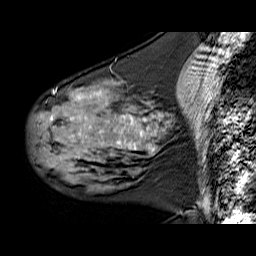
Breast MRI (dynamic contrast-enhanced), one sagittal slice. Dynamic contrast-enhanced series, time point 2 of 6 at this slice position (early post-contrast). 1.5 T. TE 6.3 ms, TR 32.9 ms. 256 × 256 image matrix, field of view 200 × 200 mm. Female patient. From the clinical record (not read from this slice): setting: breast cancer imaged before/during neoadjuvant chemotherapy; receptor status: HER2-positive.
Annotated regions visible in this slice (semi-automatically segmented with operator editing):
- analysis volume of interest (the breast-tissue region the enhancement analysis was run in; not a lesion): box from (x=31, y=79) to (x=169, y=180) px
- tumour enhancement mask (voxels above the 100 % enhancement threshold inside the analysis volume of interest): (x=51, y=93)–(x=159, y=152)